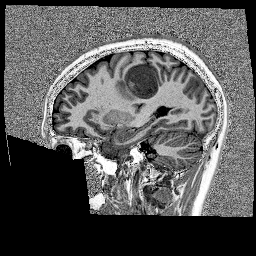
Brain MRI from a brain-tumour surgery series, one sagittal slice; slice 63 of 176 in the series (ordered by position); 1 mm slice thickness; 256 × 256 image matrix. From the clinical record (not read from this slice): histopathology: Glioblastoma; WHO grade: 4; IDH mutation: no; tumour location: Left Frontal.
Structures marked on this image (outlined manually by an expert reader):
- tumour: bounding box (x1, y1, x2, y2) in pixels: (118, 58, 175, 95)